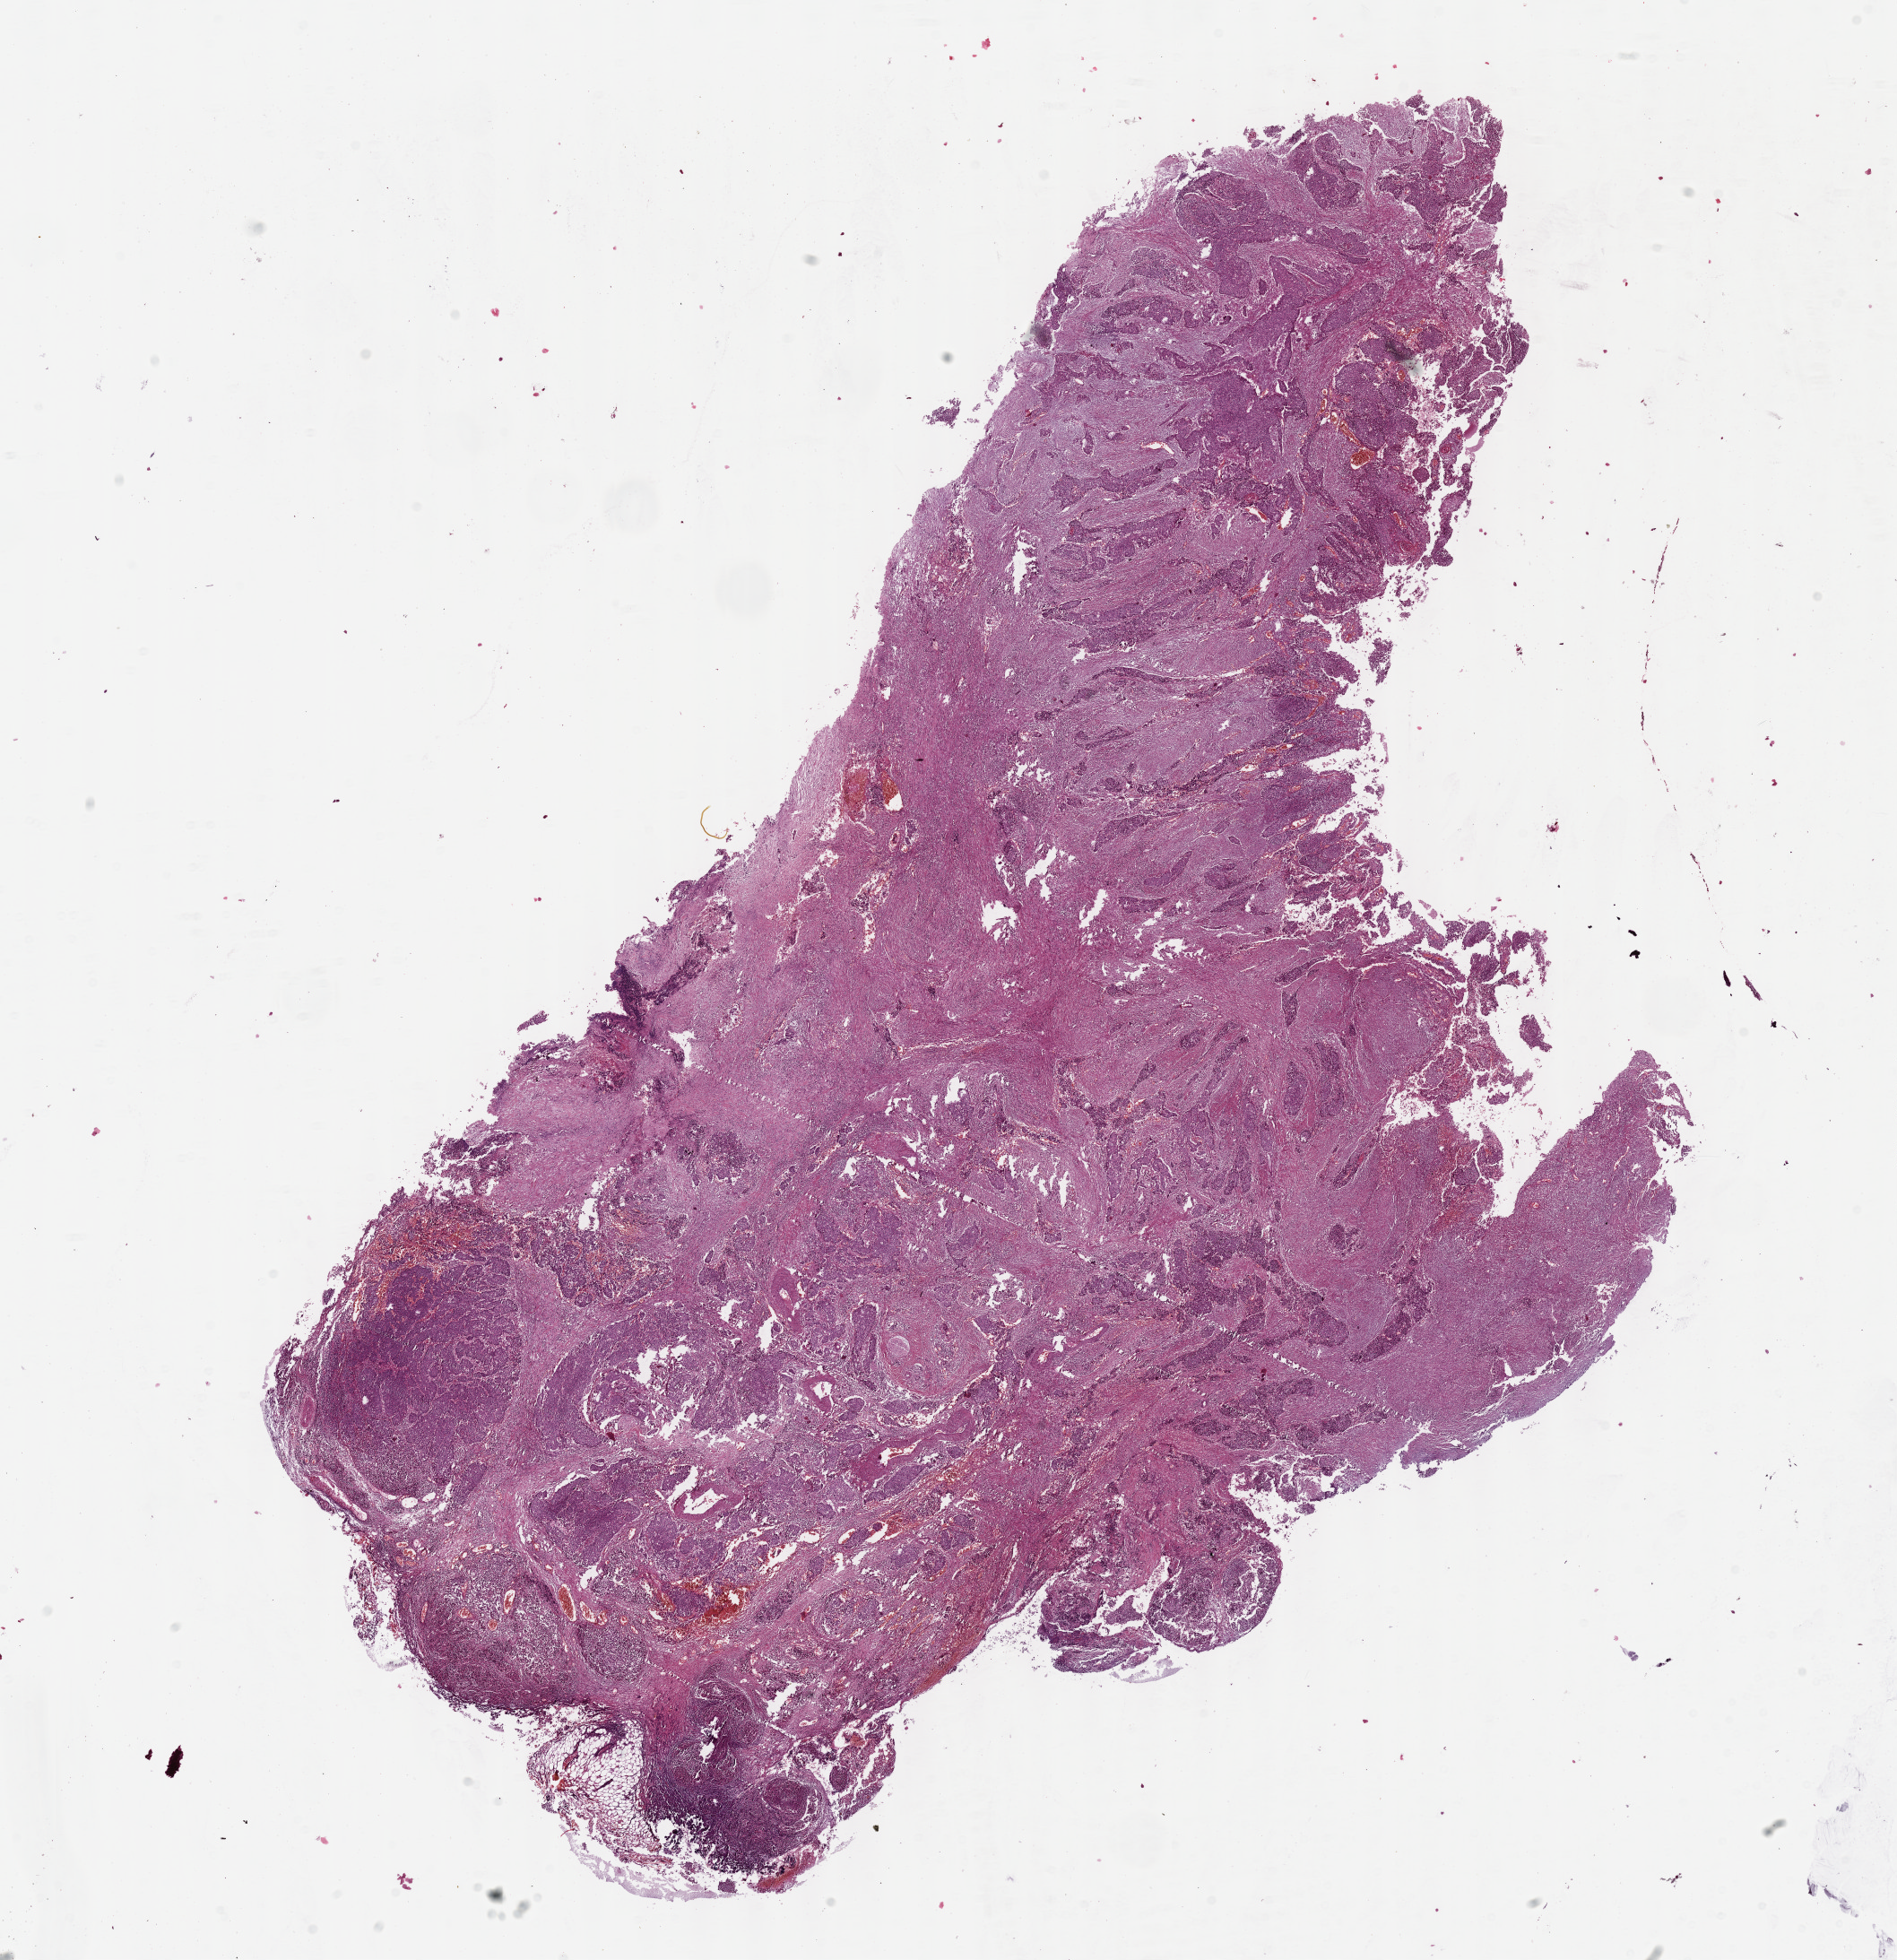
Digitized H&E tissue section (whole slide), a low-resolution overview of the entire scanned area, about 17.1 x 17.7 mm (from a 40x scan), formalin-fixed paraffin-embedded (FFPE) diagnostic section, primary tumour sample from the esophagus. Male, age 49 years at initial diagnosis. Histologic grade: G2 (moderately differentiated).
Diagnosis: Squamous cell carcinoma, NOS (upper third of esophagus). TNM: T2 N0 M0. AJCC pathologic stage: IIA (6th edition).